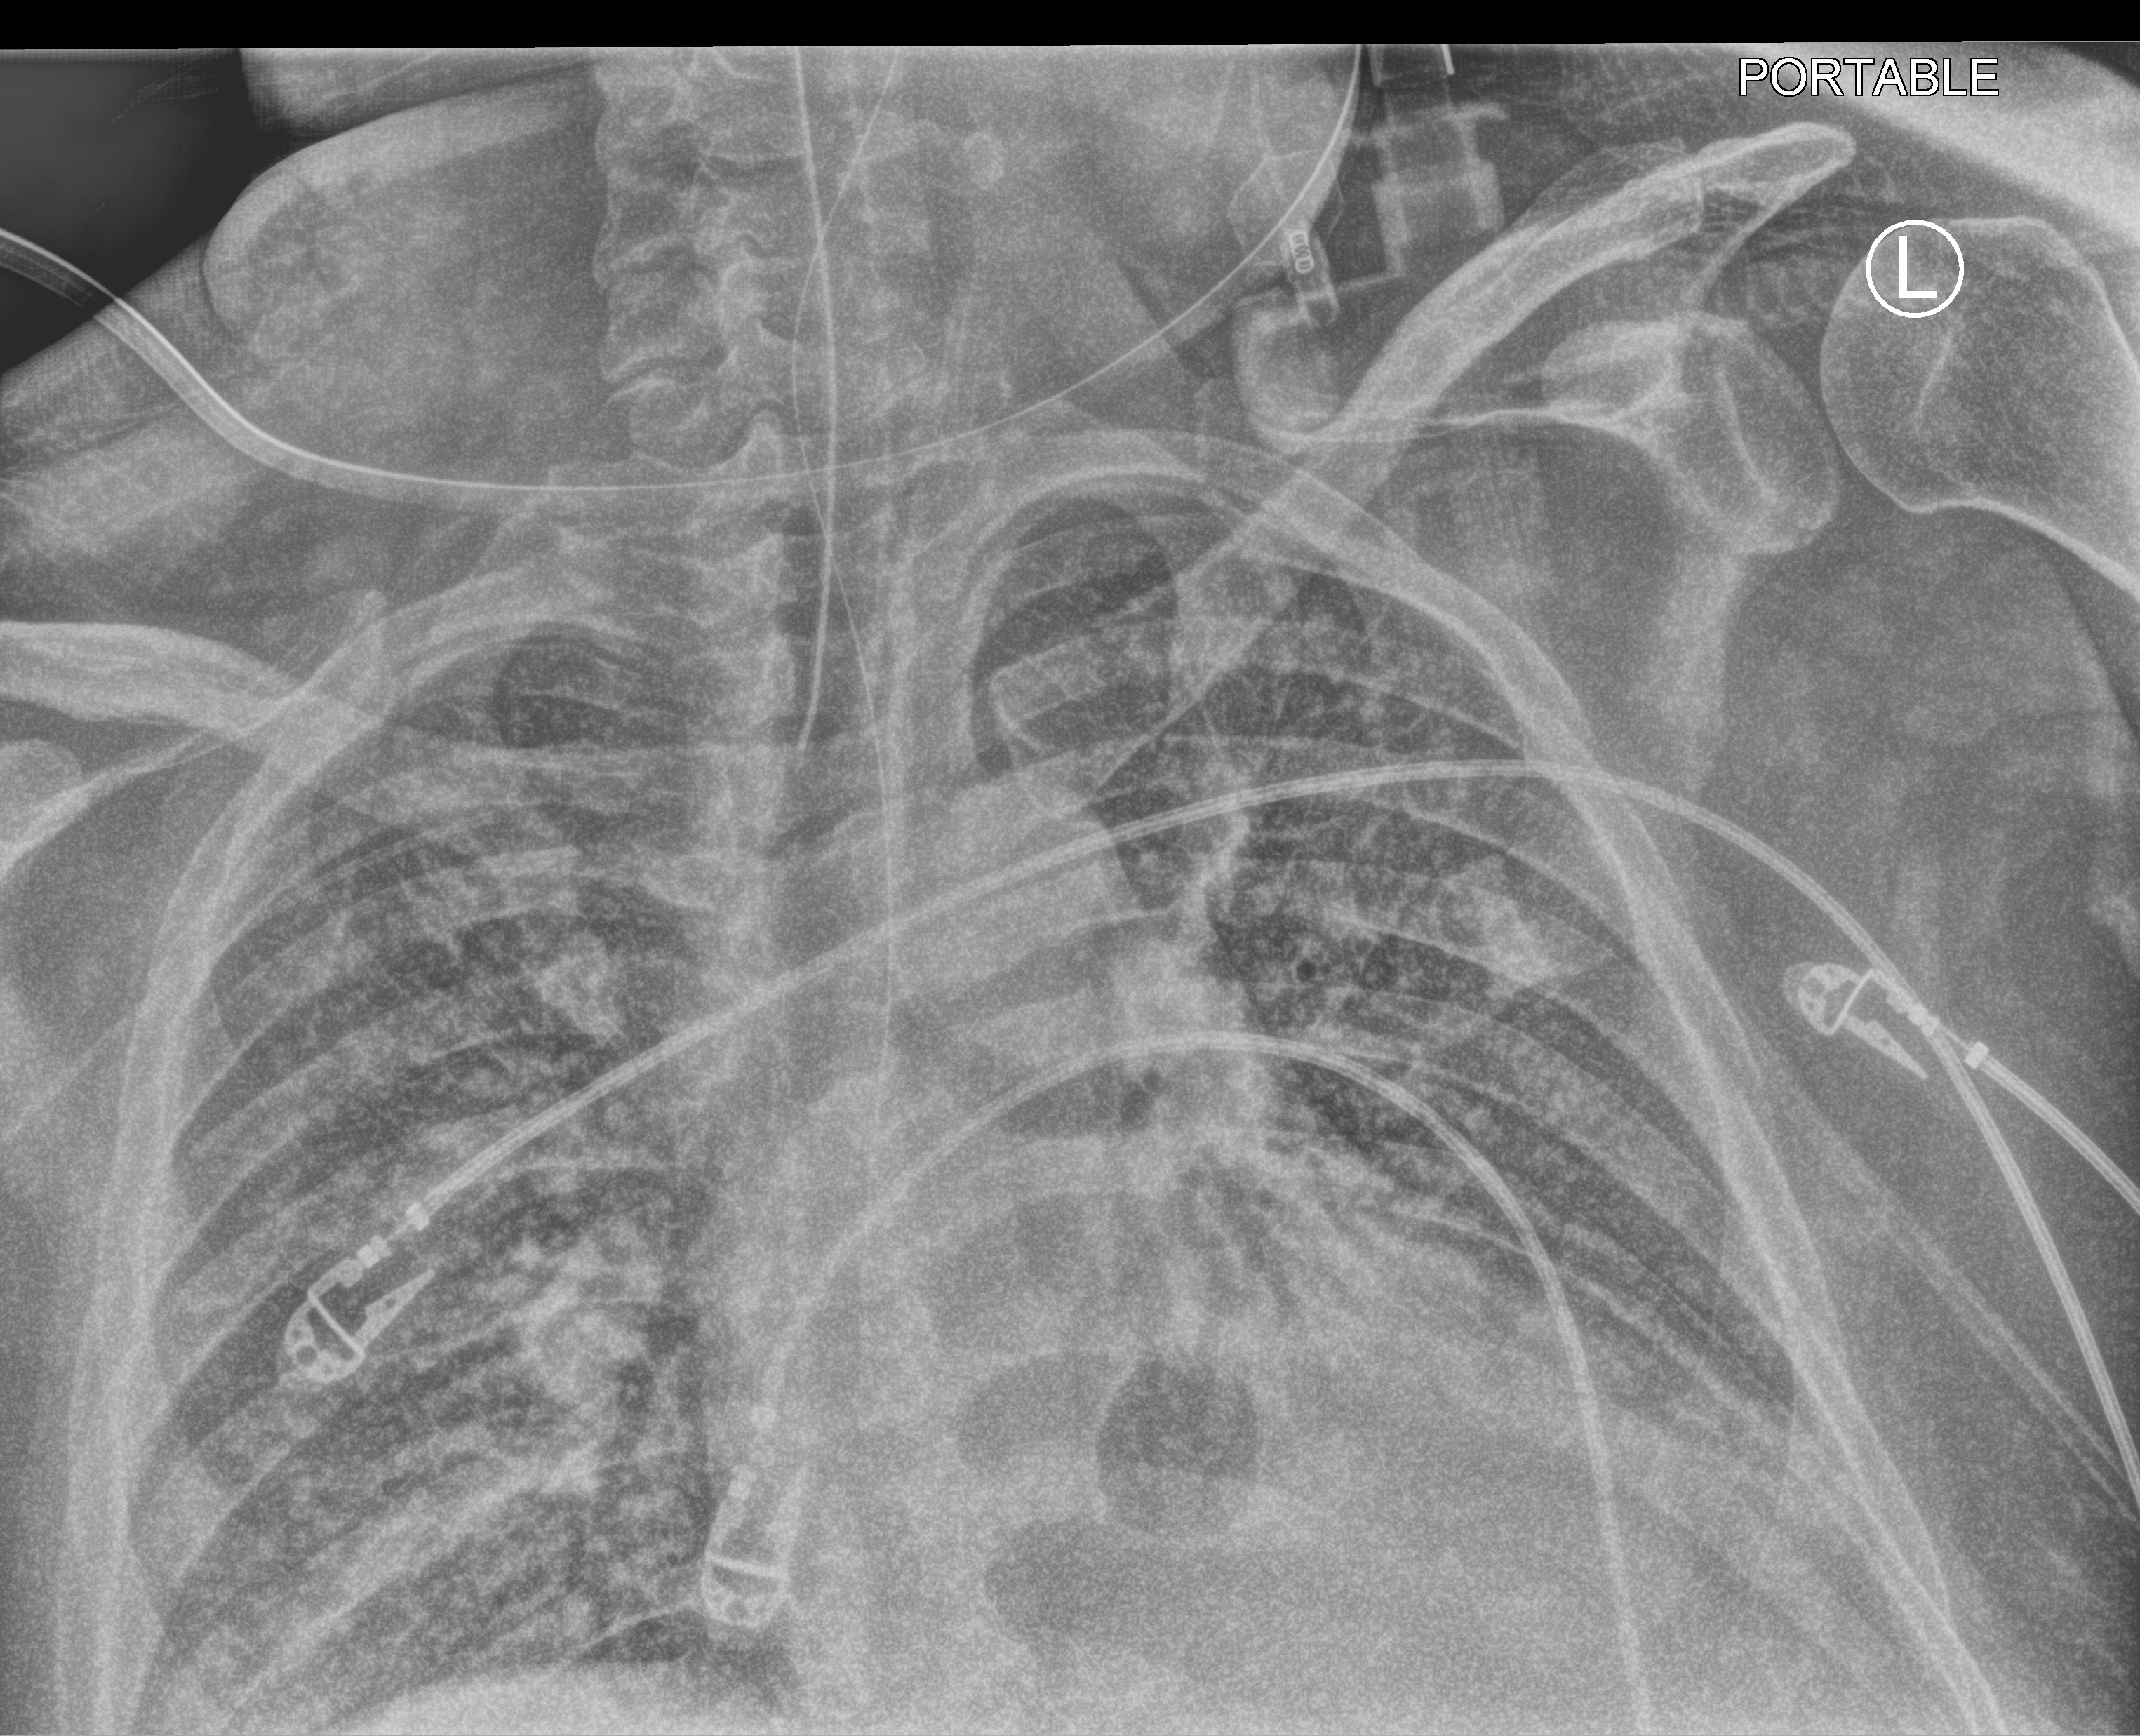
Chest X-ray (portable); anteroposterior (AP) projection. Adult patient hospitalised with COVID-19, age 18–59 years.
From the hospital-stay record, not from the radiograph (when in the stay this image was taken is not recorded):
- diabetes (admission record): yes
- admitted to intensive care during this hospital stay: yes
- chronic kidney disease (admission record): no